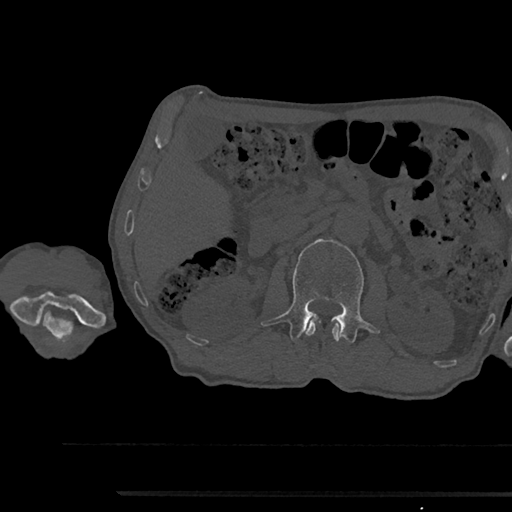
CT including the spine, one axial slice. Position 586 of 797 along the scan axis. Reconstruction kernel Br40s/3. Bone window (W 1800 / L 400 HU). 0.5 mm slice thickness. 512 × 512 image matrix. Patient: male, 79 years. From the clinical record (not read from this slice): primary cancer: prostate.
Structures marked on this image (semi-automatically segmented with operator editing):
- L1 vertebra: bounding box (x1, y1, x2, y2) in pixels: (305, 319, 341, 342)
- L2 vertebra: (260, 239, 379, 342)